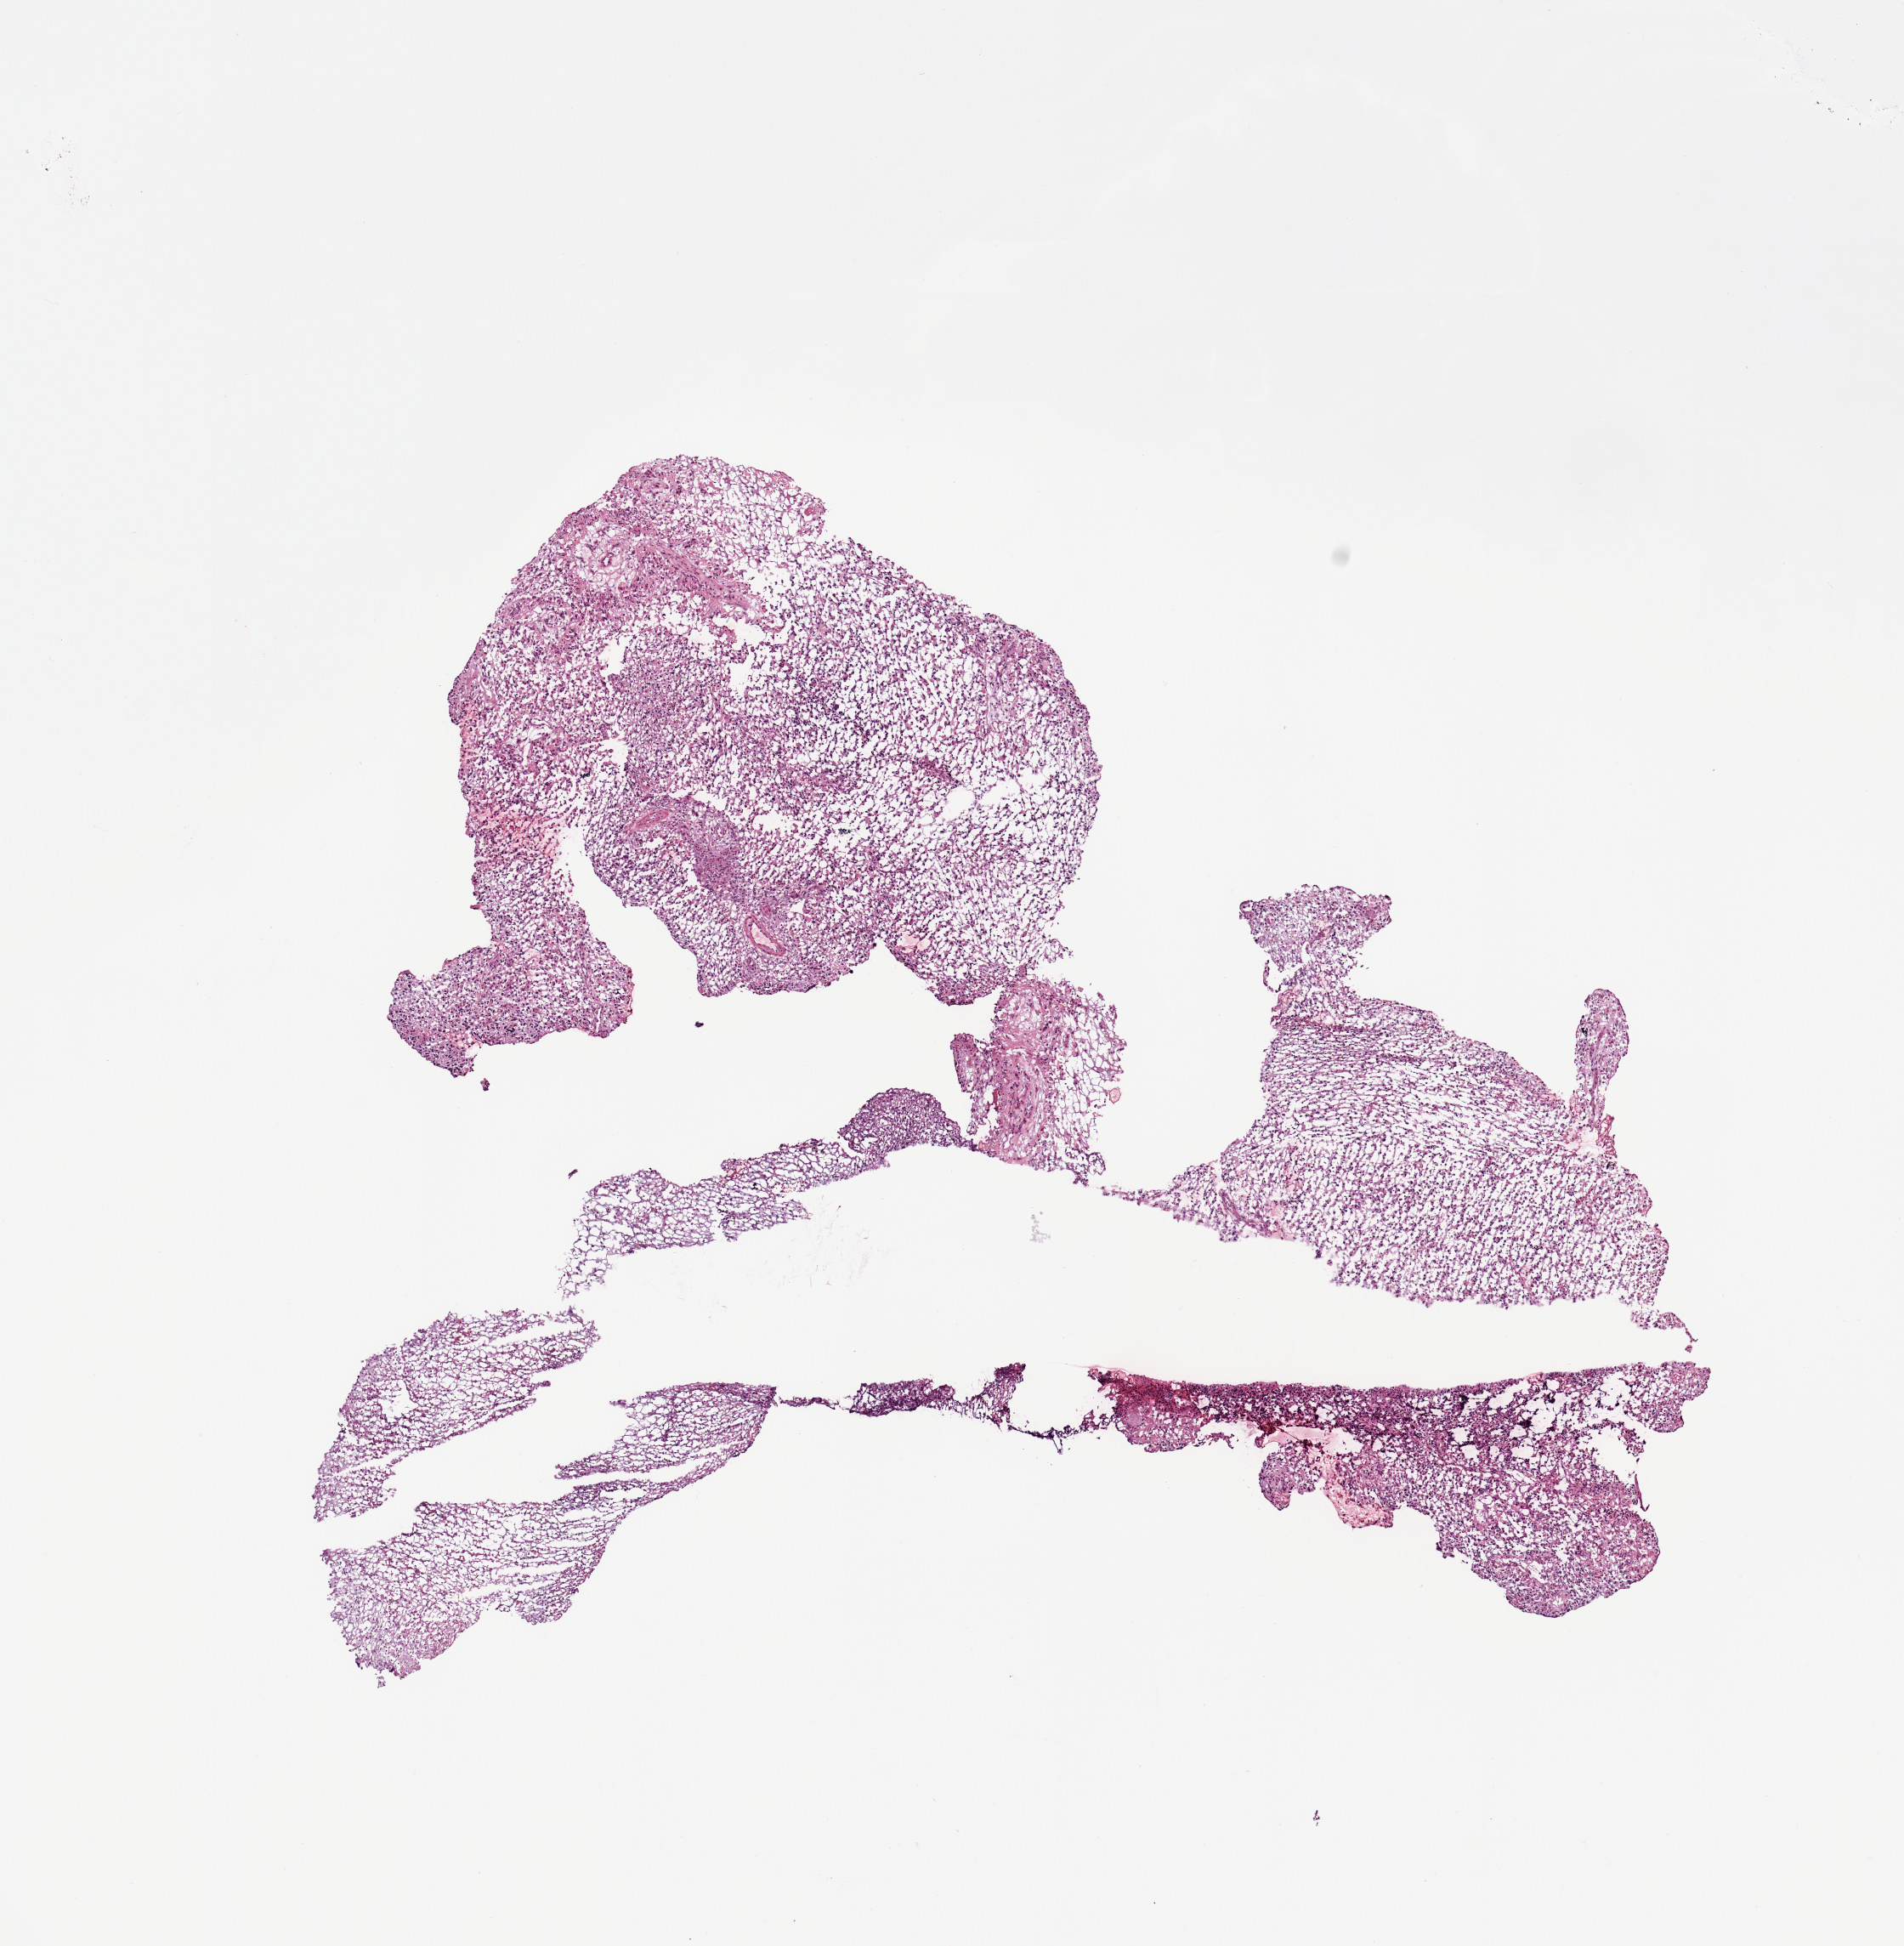
Digitized Hematoxylin and eosin (H&E) stained tissue section (whole slide), a low-resolution overview of the entire scanned area, about 8.9 x 9.1 mm (from a 20x scan); brain, tumour tissue. Patient: male, age 68 years.
Primary tumour site (as recorded): occipital lobe. Patient diagnosis (cohort enrolment): glioblastoma multiforme (brain).